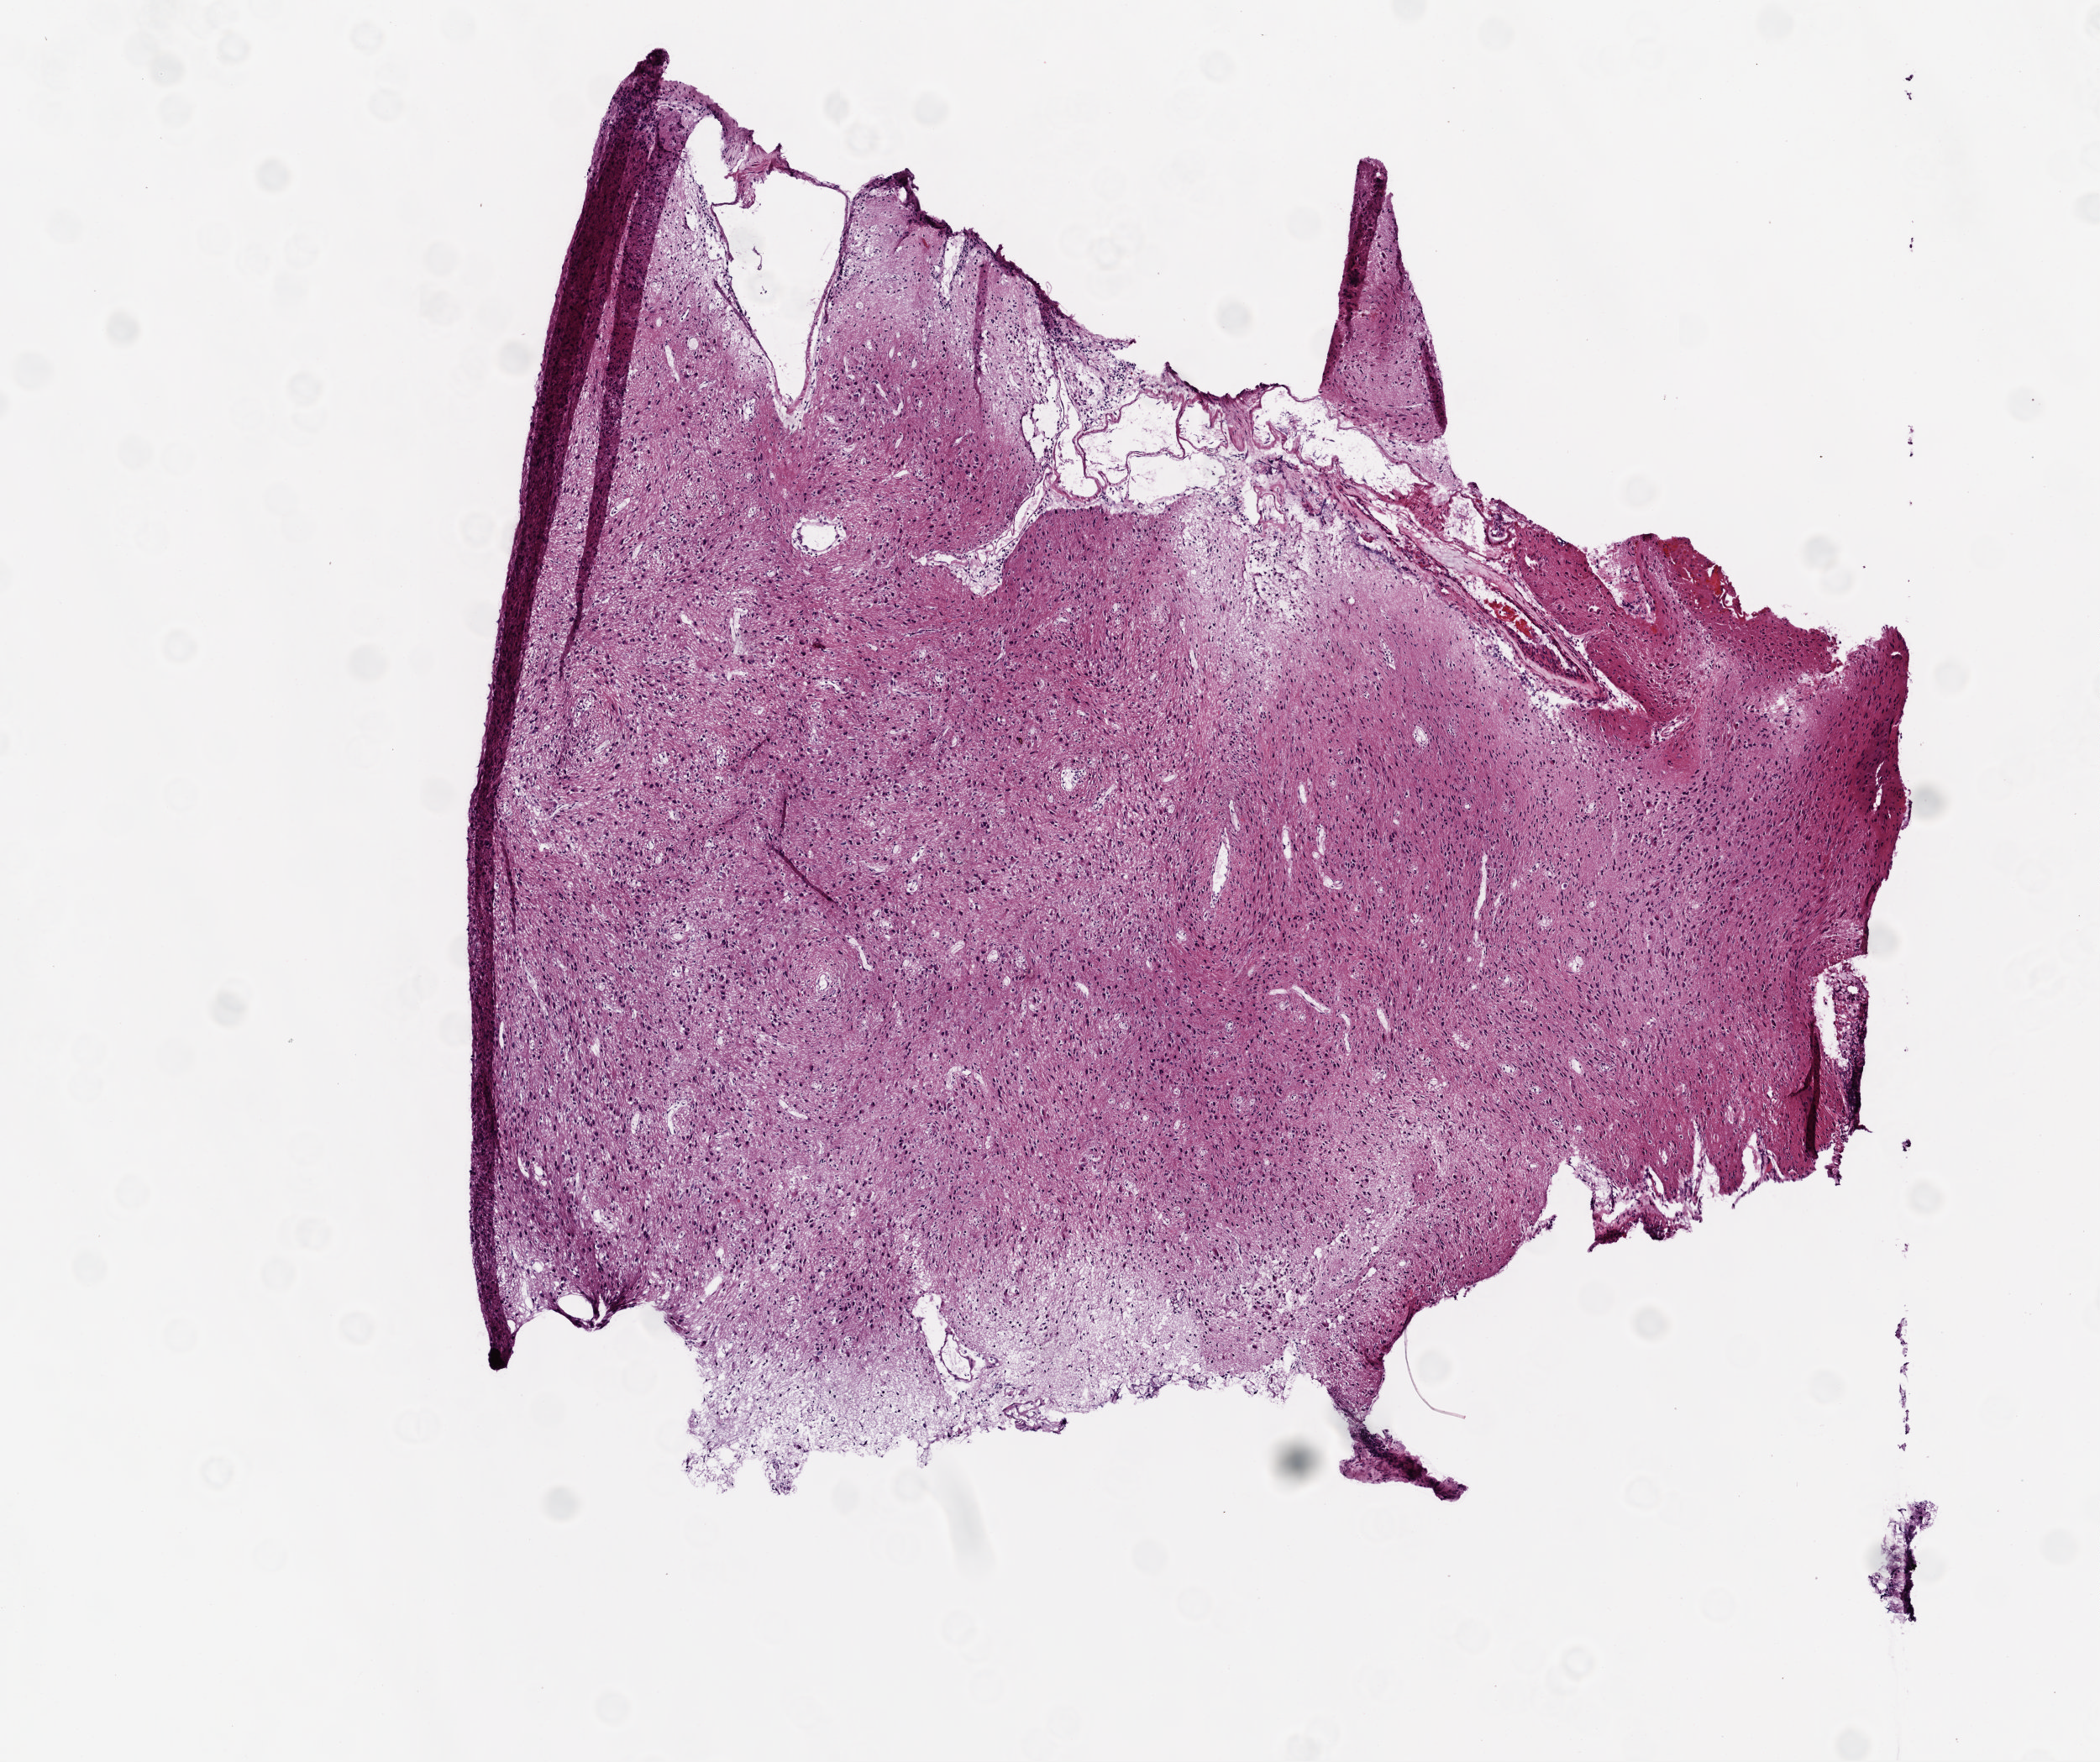
H&E-stained whole-slide image — low-resolution overview of the scanned area, about 5.0 x 4.2 mm (acquisition: 20x scan). Frozen section from the top of the tissue portion. Brain, primary tumour sample. Male patient; age at initial diagnosis 73 years. Pathologist review of this section (percent, as recorded): tumour cells 100%, tumour nuclei 80%, normal cells 0%, stromal cells 0%, necrosis 0%.
* histologic diagnosis: Glioblastoma